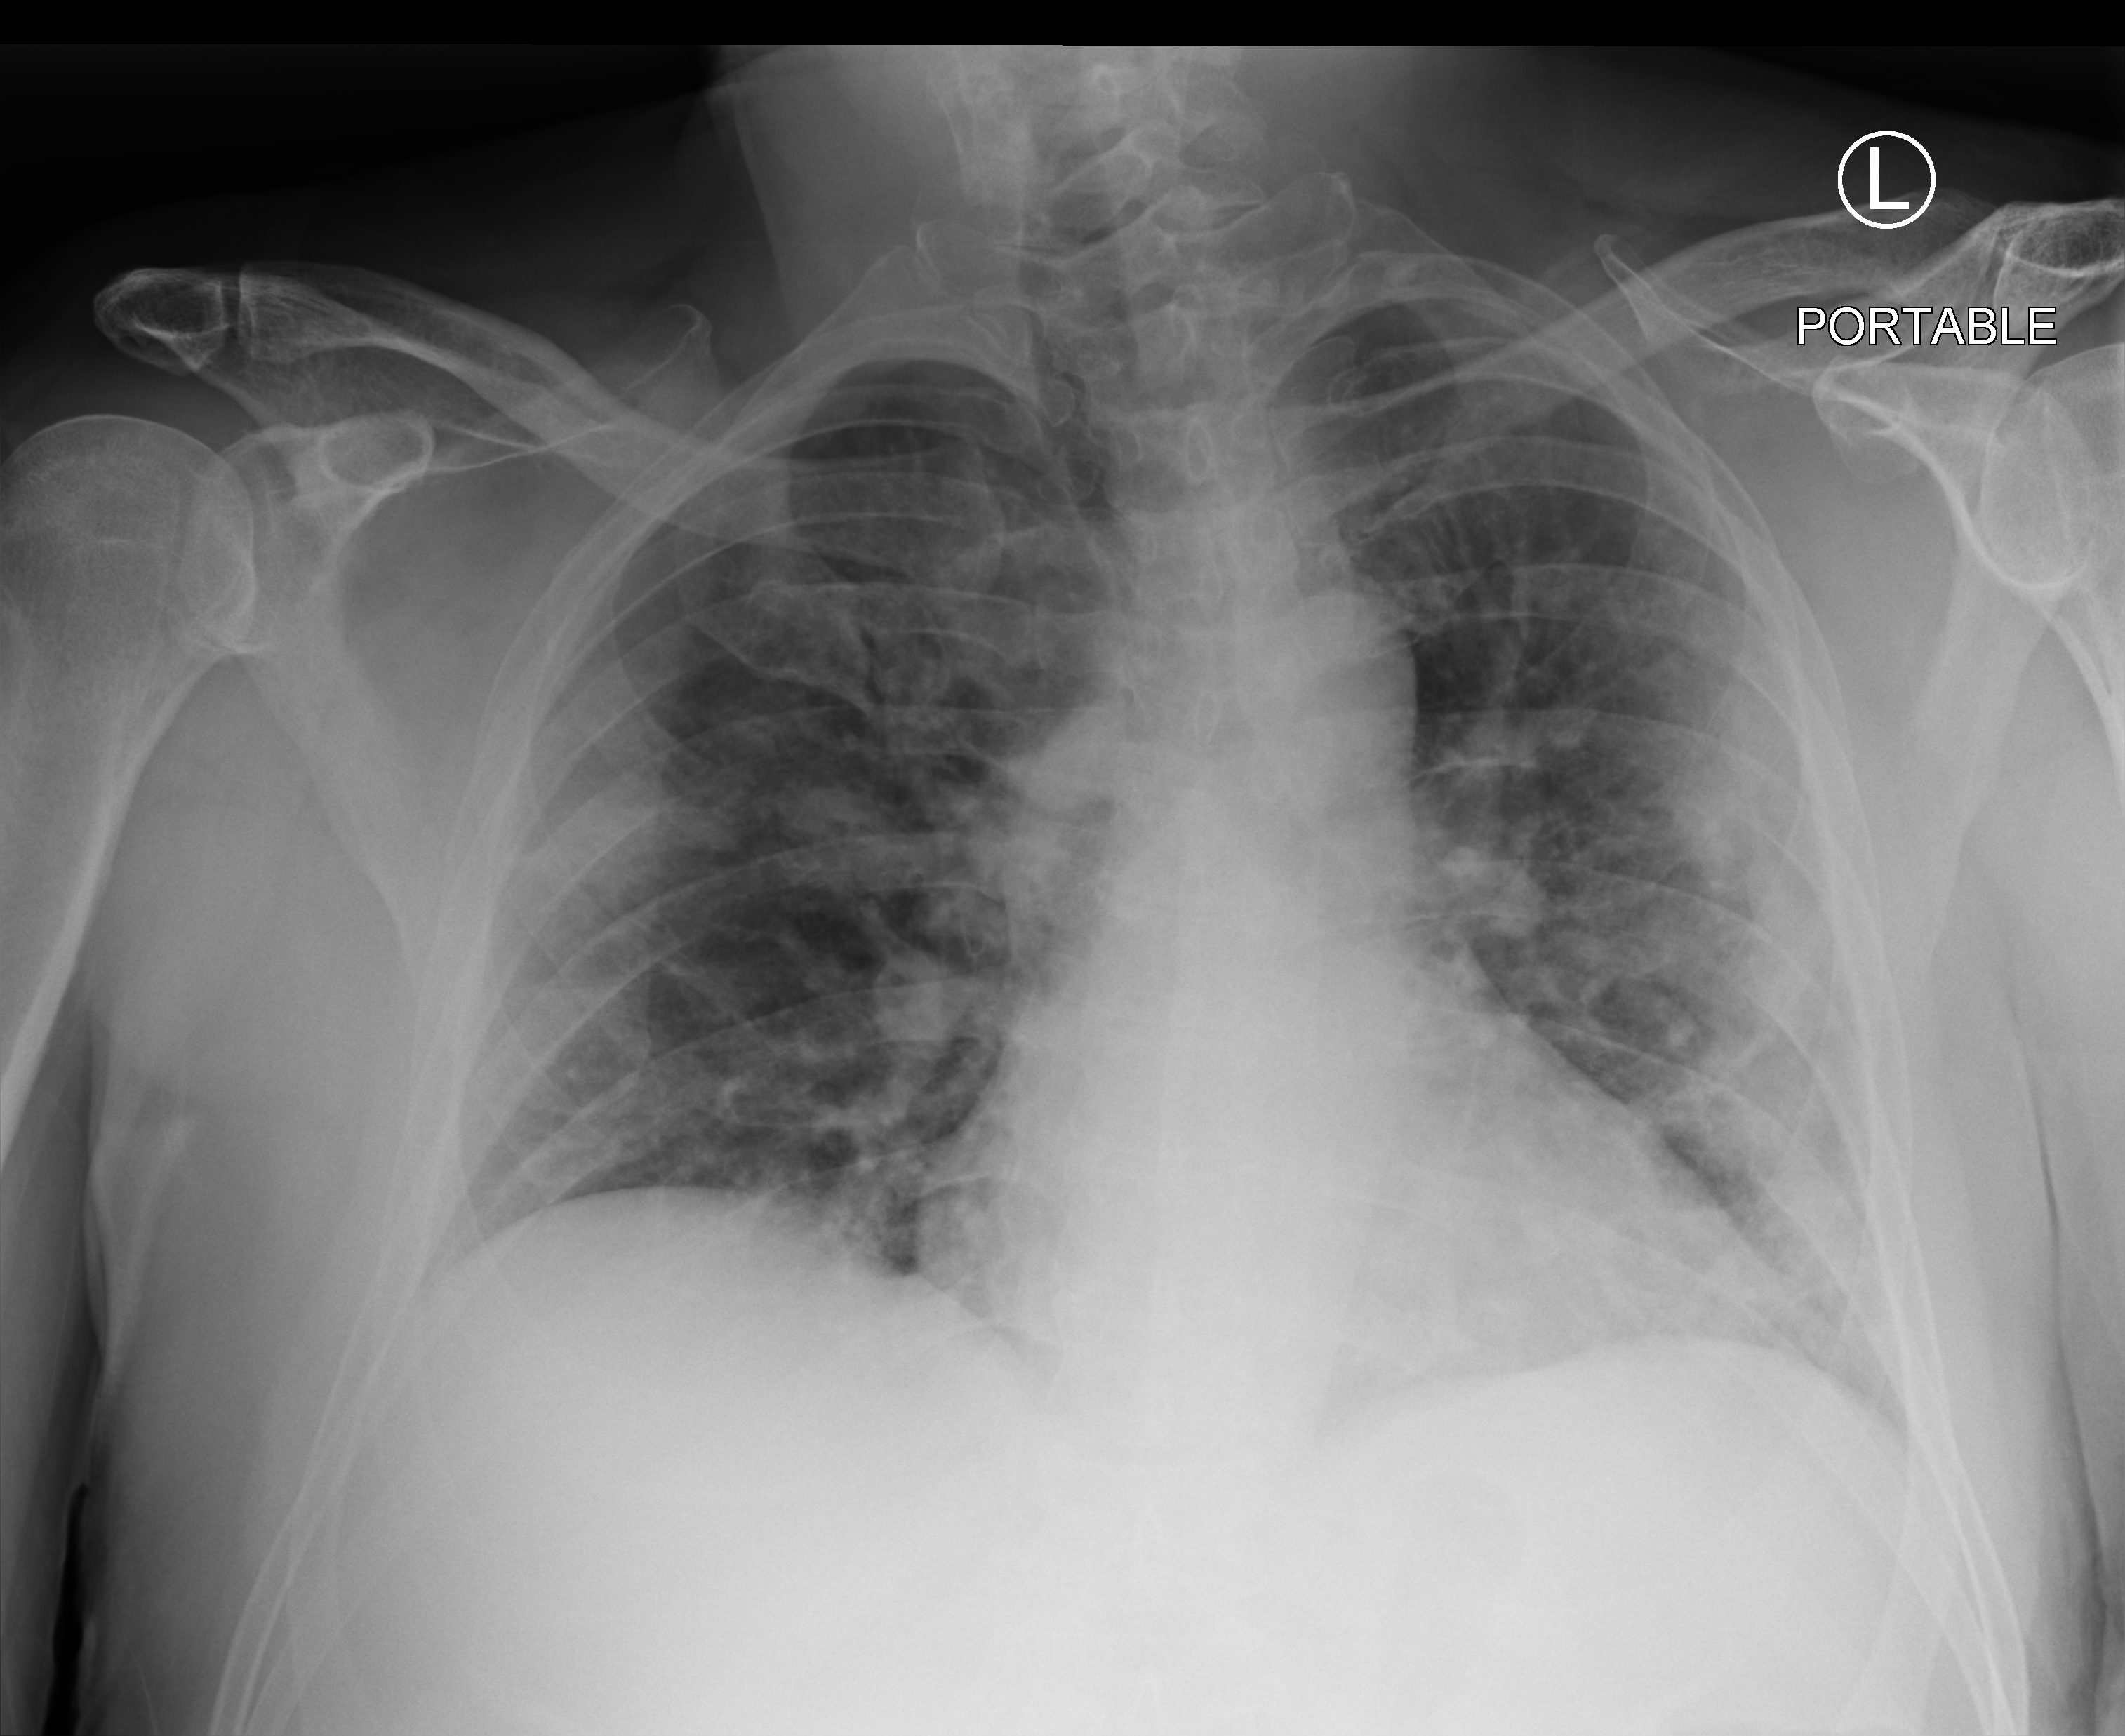
Portable chest radiograph; anteroposterior (AP) projection. Male patient hospitalised with COVID-19, age 18–59 years.
From the hospital-stay record, not from the radiograph (when in the stay this image was taken is not recorded): hypertension (admission record): yes; admitted to intensive care during this hospital stay: yes.